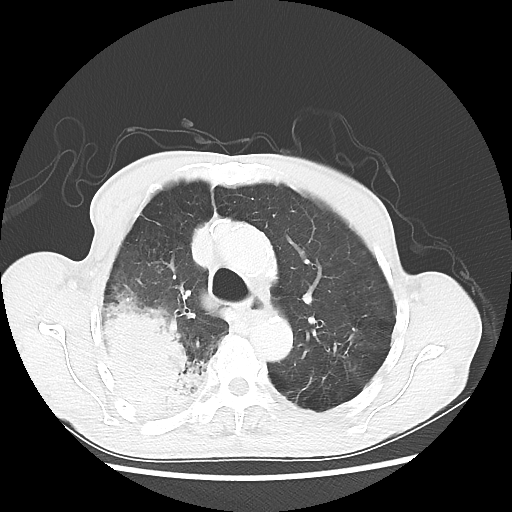
Chest CT, one axial slice. Slice 39 of 58 in the series (ordered by position). Lung window (W 1500 / L -600 HU). 5 mm slice thickness. 512 × 512 image matrix. Male patient, age 75 years. From the clinical record (not read from this slice): clinical TNM (as recorded): T4 N1 M1.
Annotated regions visible in this slice (bounding box drawn by a radiologist):
- lung tumour (recorded histology: adenocarcinoma): box from (x=96, y=288) to (x=212, y=418) px